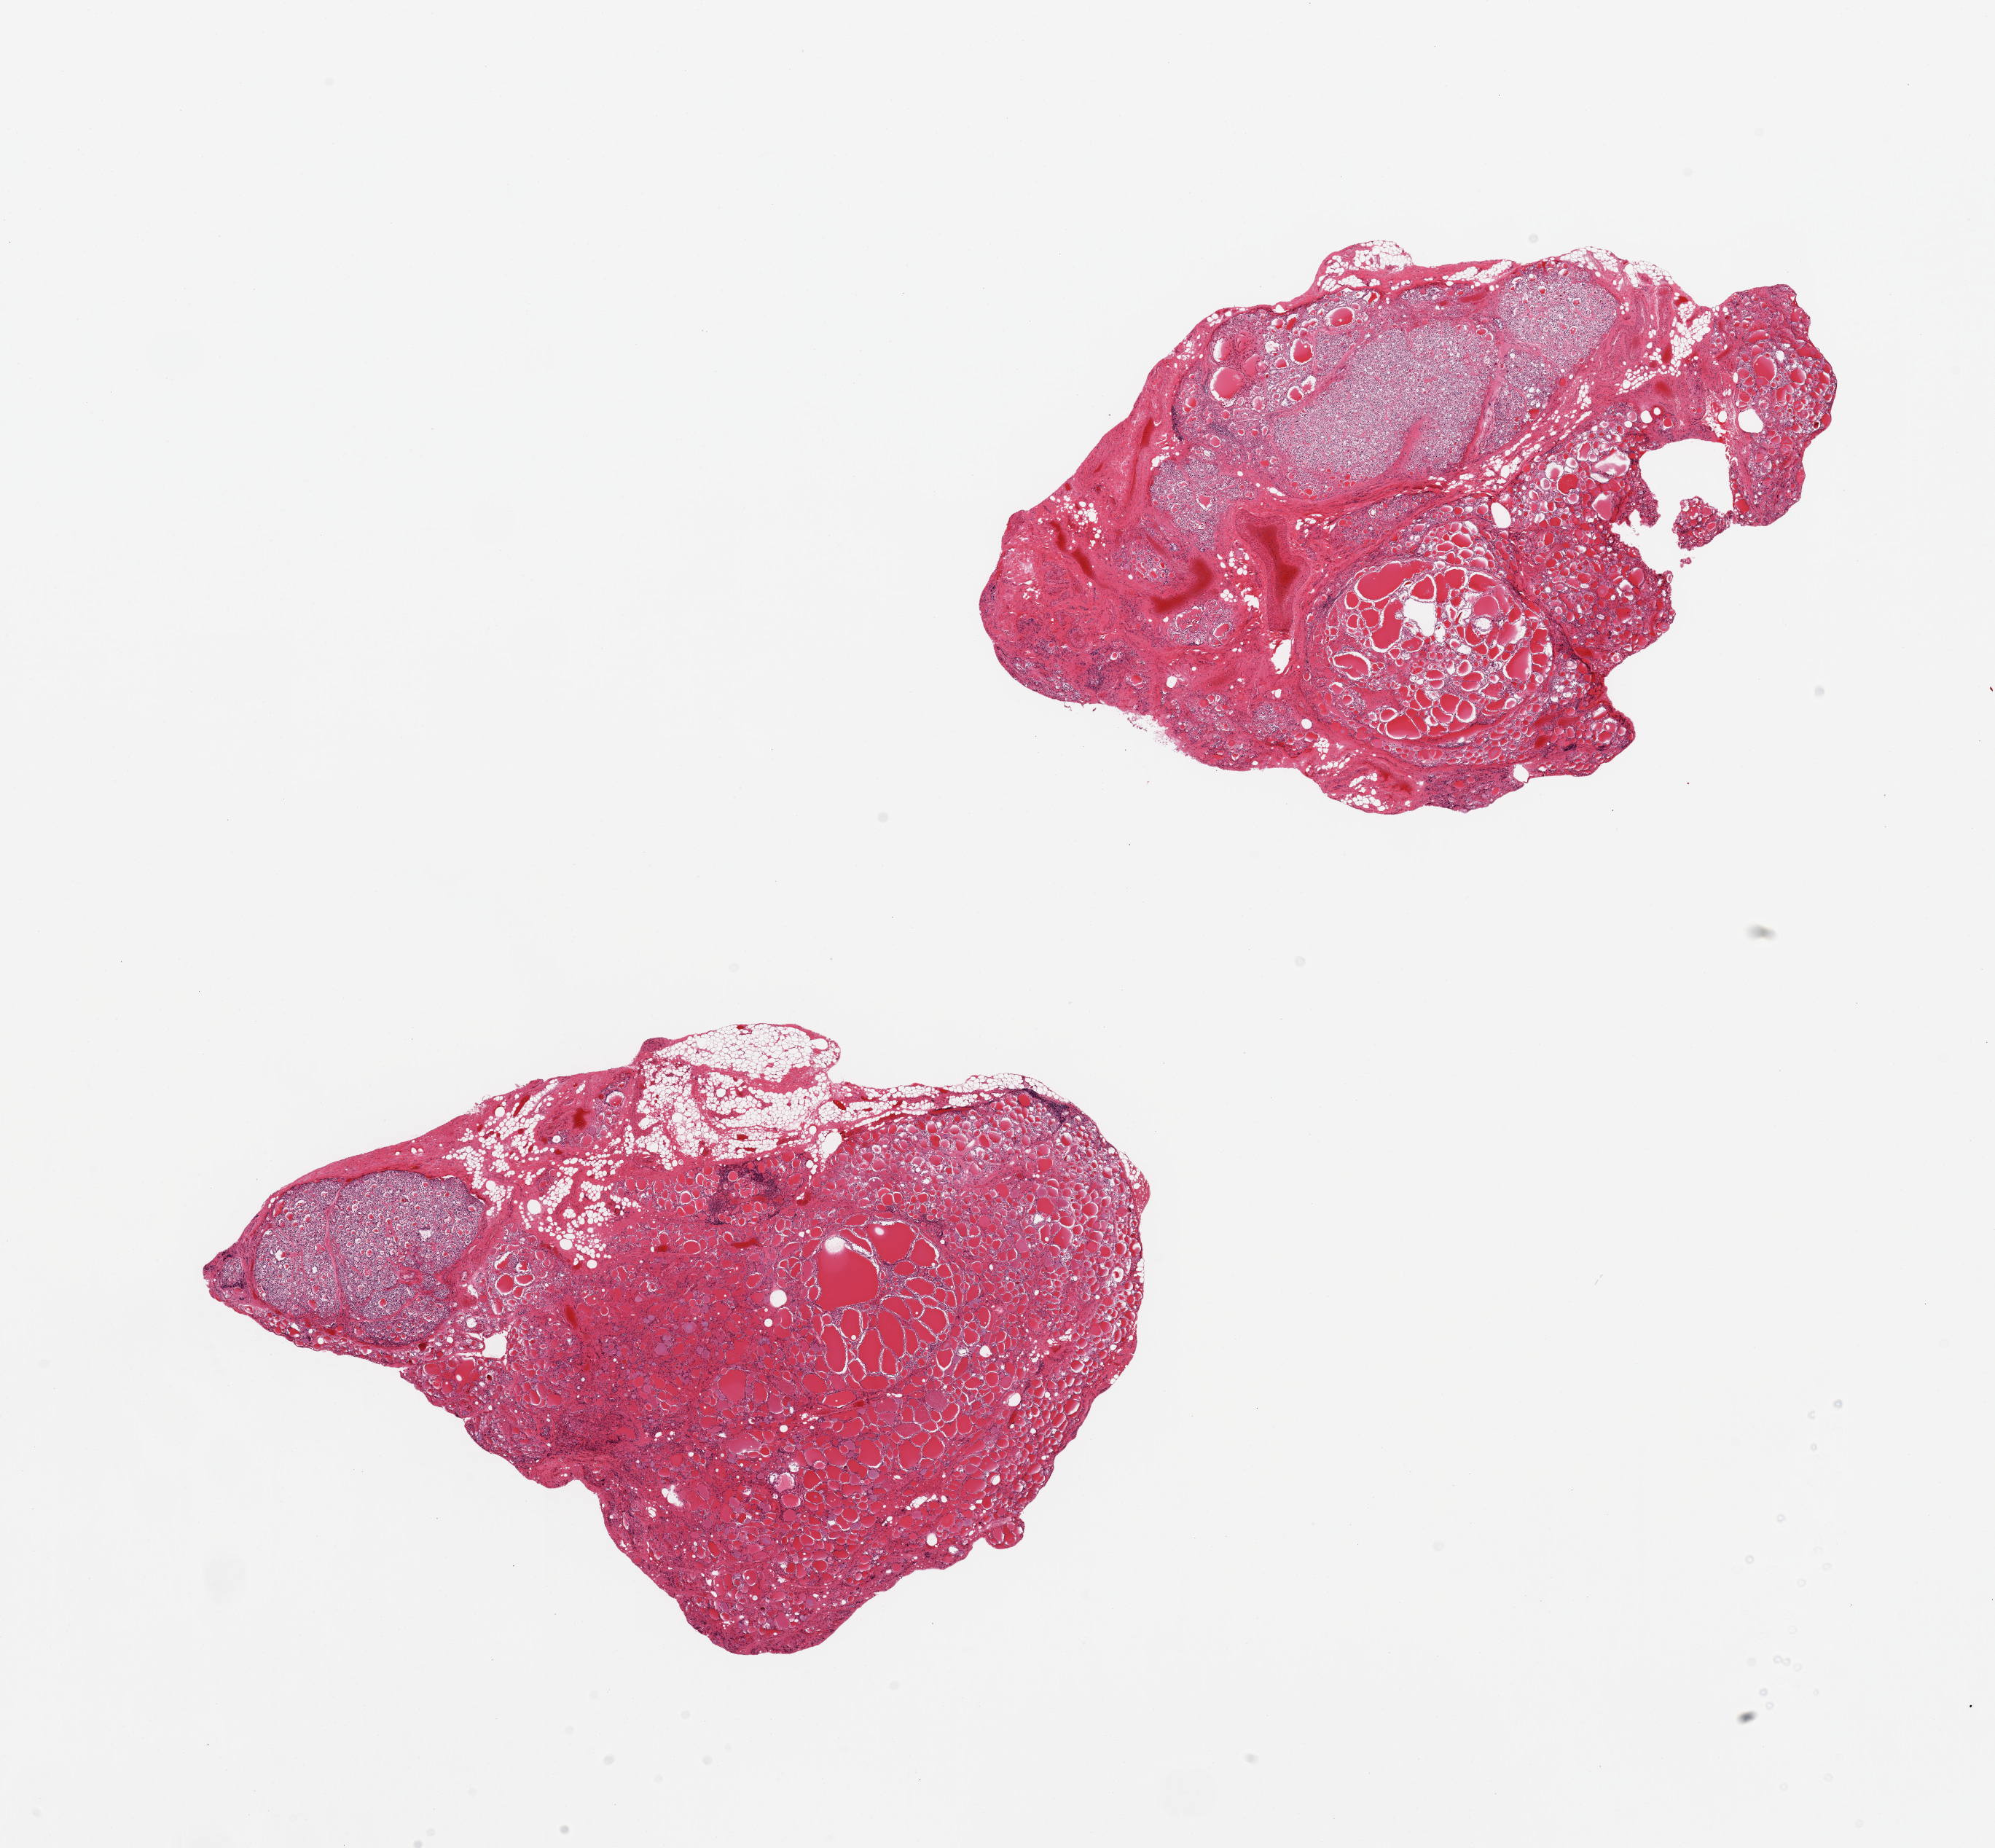
Haematoxylin and eosin whole-slide image, a low-resolution overview of the entire scanned area, about 21.7 x 20.1 mm (slide scanned at 20x), PAXgene-fixed, paraffin-embedded tissue, section of thyroid (target tissue), donor tissue sample. Donor: female.
* pathologist's review note for this sample: 2 pieces; microfollicular adenomatous nodules; 15% external fat on 1 piece